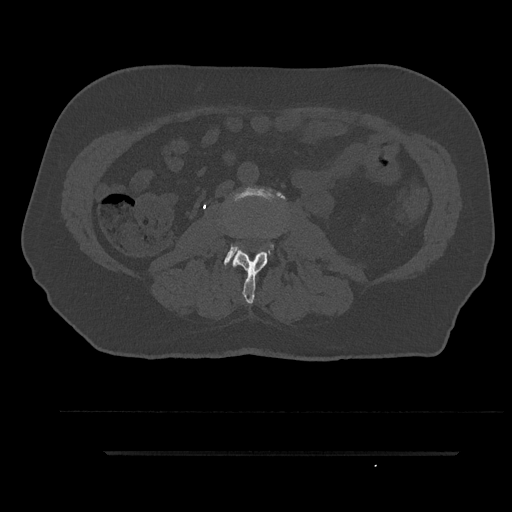
CT including the spine, one axial slice. Reconstruction kernel Br40s/3. Bone window (W 1800 / L 400 HU). 512 × 512 image matrix, field of view 432 × 432 mm. Patient: male, 63 years. Case-level facts recorded for this patient, not image findings: primary cancer: renal.
Outlined on this slice (semi-automatically segmented with operator editing):
- L2 vertebra: box from (x=232, y=251) to (x=268, y=304) px
- L3 vertebra: (x=224, y=188)–(x=284, y=265)